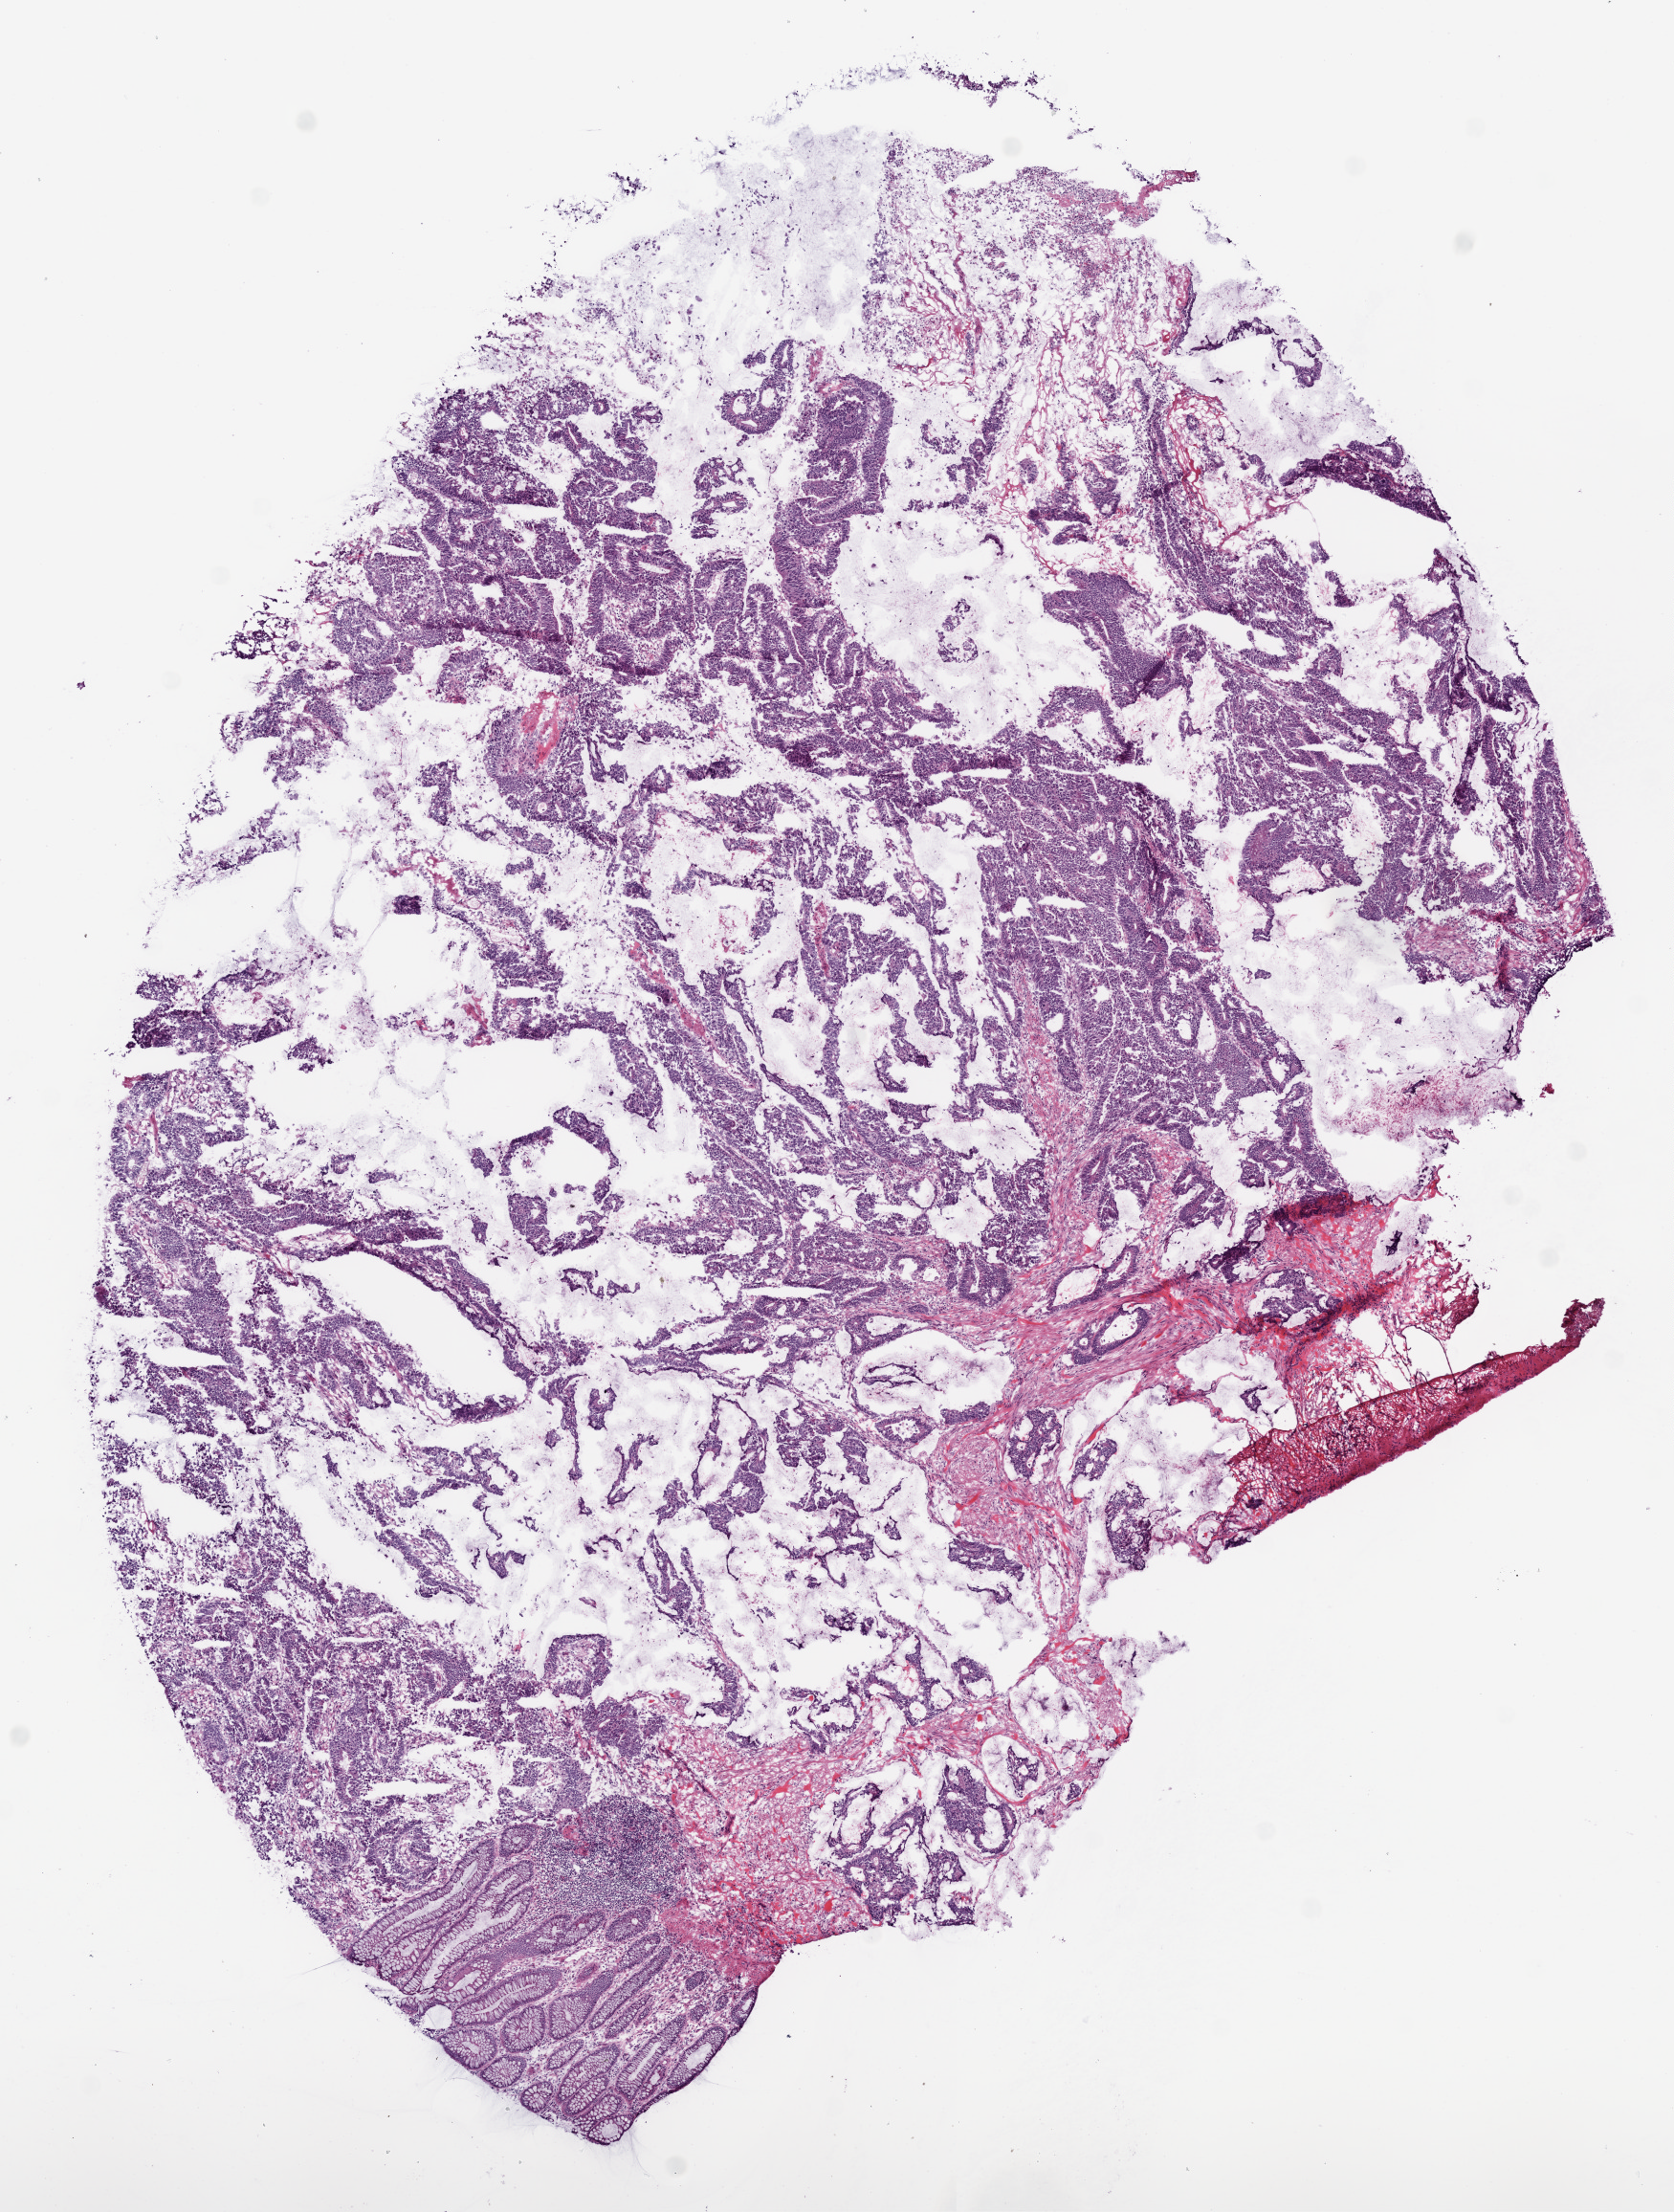
Hematoxylin and eosin (H&E) stained whole-slide image — low-resolution overview of the scanned area, about 7.0 x 9.3 mm (from a 20x scan), frozen section from the bottom of the tissue portion, primary tumour sample from the colon. Female, age 47 years at initial diagnosis. Pathologist review of this section (percent, as recorded): tumour cells 79%, tumour nuclei 70%, normal cells 5%, stromal cells 8%, necrosis 8%.
* AJCC pathologic stage: IV (6th edition)
* diagnosis: Mucinous adenocarcinoma
* TNM: T3 N2 M1
* lymph nodes positive (case pathology): 5 of 30 examined